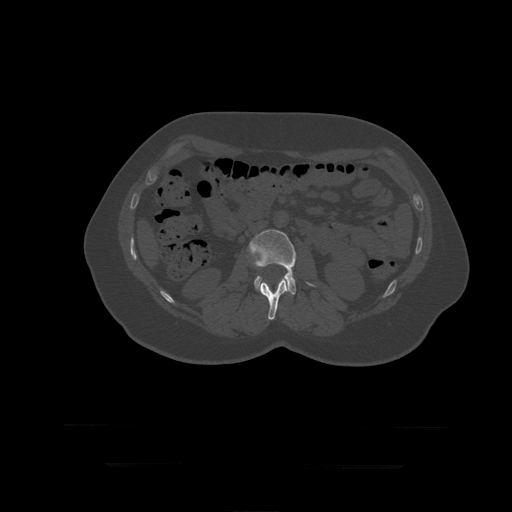
CT including the spine, one axial slice. Position 136 of 399 along the scan axis. Reconstruction kernel STANDARD. 120 kVp. Bone window (W 1800 / L 400 HU). 512 × 512 image matrix. Patient age 41 years. From the clinical record (not read from this slice): primary cancer: breast.
Outlined on this slice (semi-automatic segmentation, software-assisted and operator-edited):
- L2 vertebra: bounding box <260,279,289,320> (left, top, right, bottom; pixels)
- L3 vertebra: <248,230,316,295>